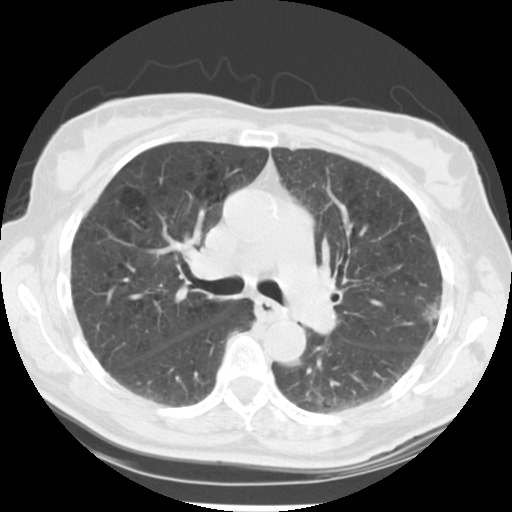
Chest CT (low-dose screening protocol), one axial image. Second annual screen. Lung window (W 1500 / L -600 HU). Slice 136 of 223 in the series. Female participant, aged 61 years at enrolment. Current smoker at enrolment.
Expert reader's lesion annotation, box from (x=406, y=282) to (x=464, y=343) px. Screening reader's record for this exam (one nodule recorded; not confirmed to be the boxed lesion): non-calcified nodule or mass ≥4 mm, left upper lobe, 15 × 15 mm, poorly defined margins, mixed attenuation, pre-existing on the prior screen: no. Official screen result: positive, other. Participant outcome: lung cancer diagnosed 152 days after this screen — bronchiolo-alveolar adenocarcinoma, NOS, left upper lobe, well differentiated (G1), stage IA (AJCC 6th edition), 11 mm at pathology.